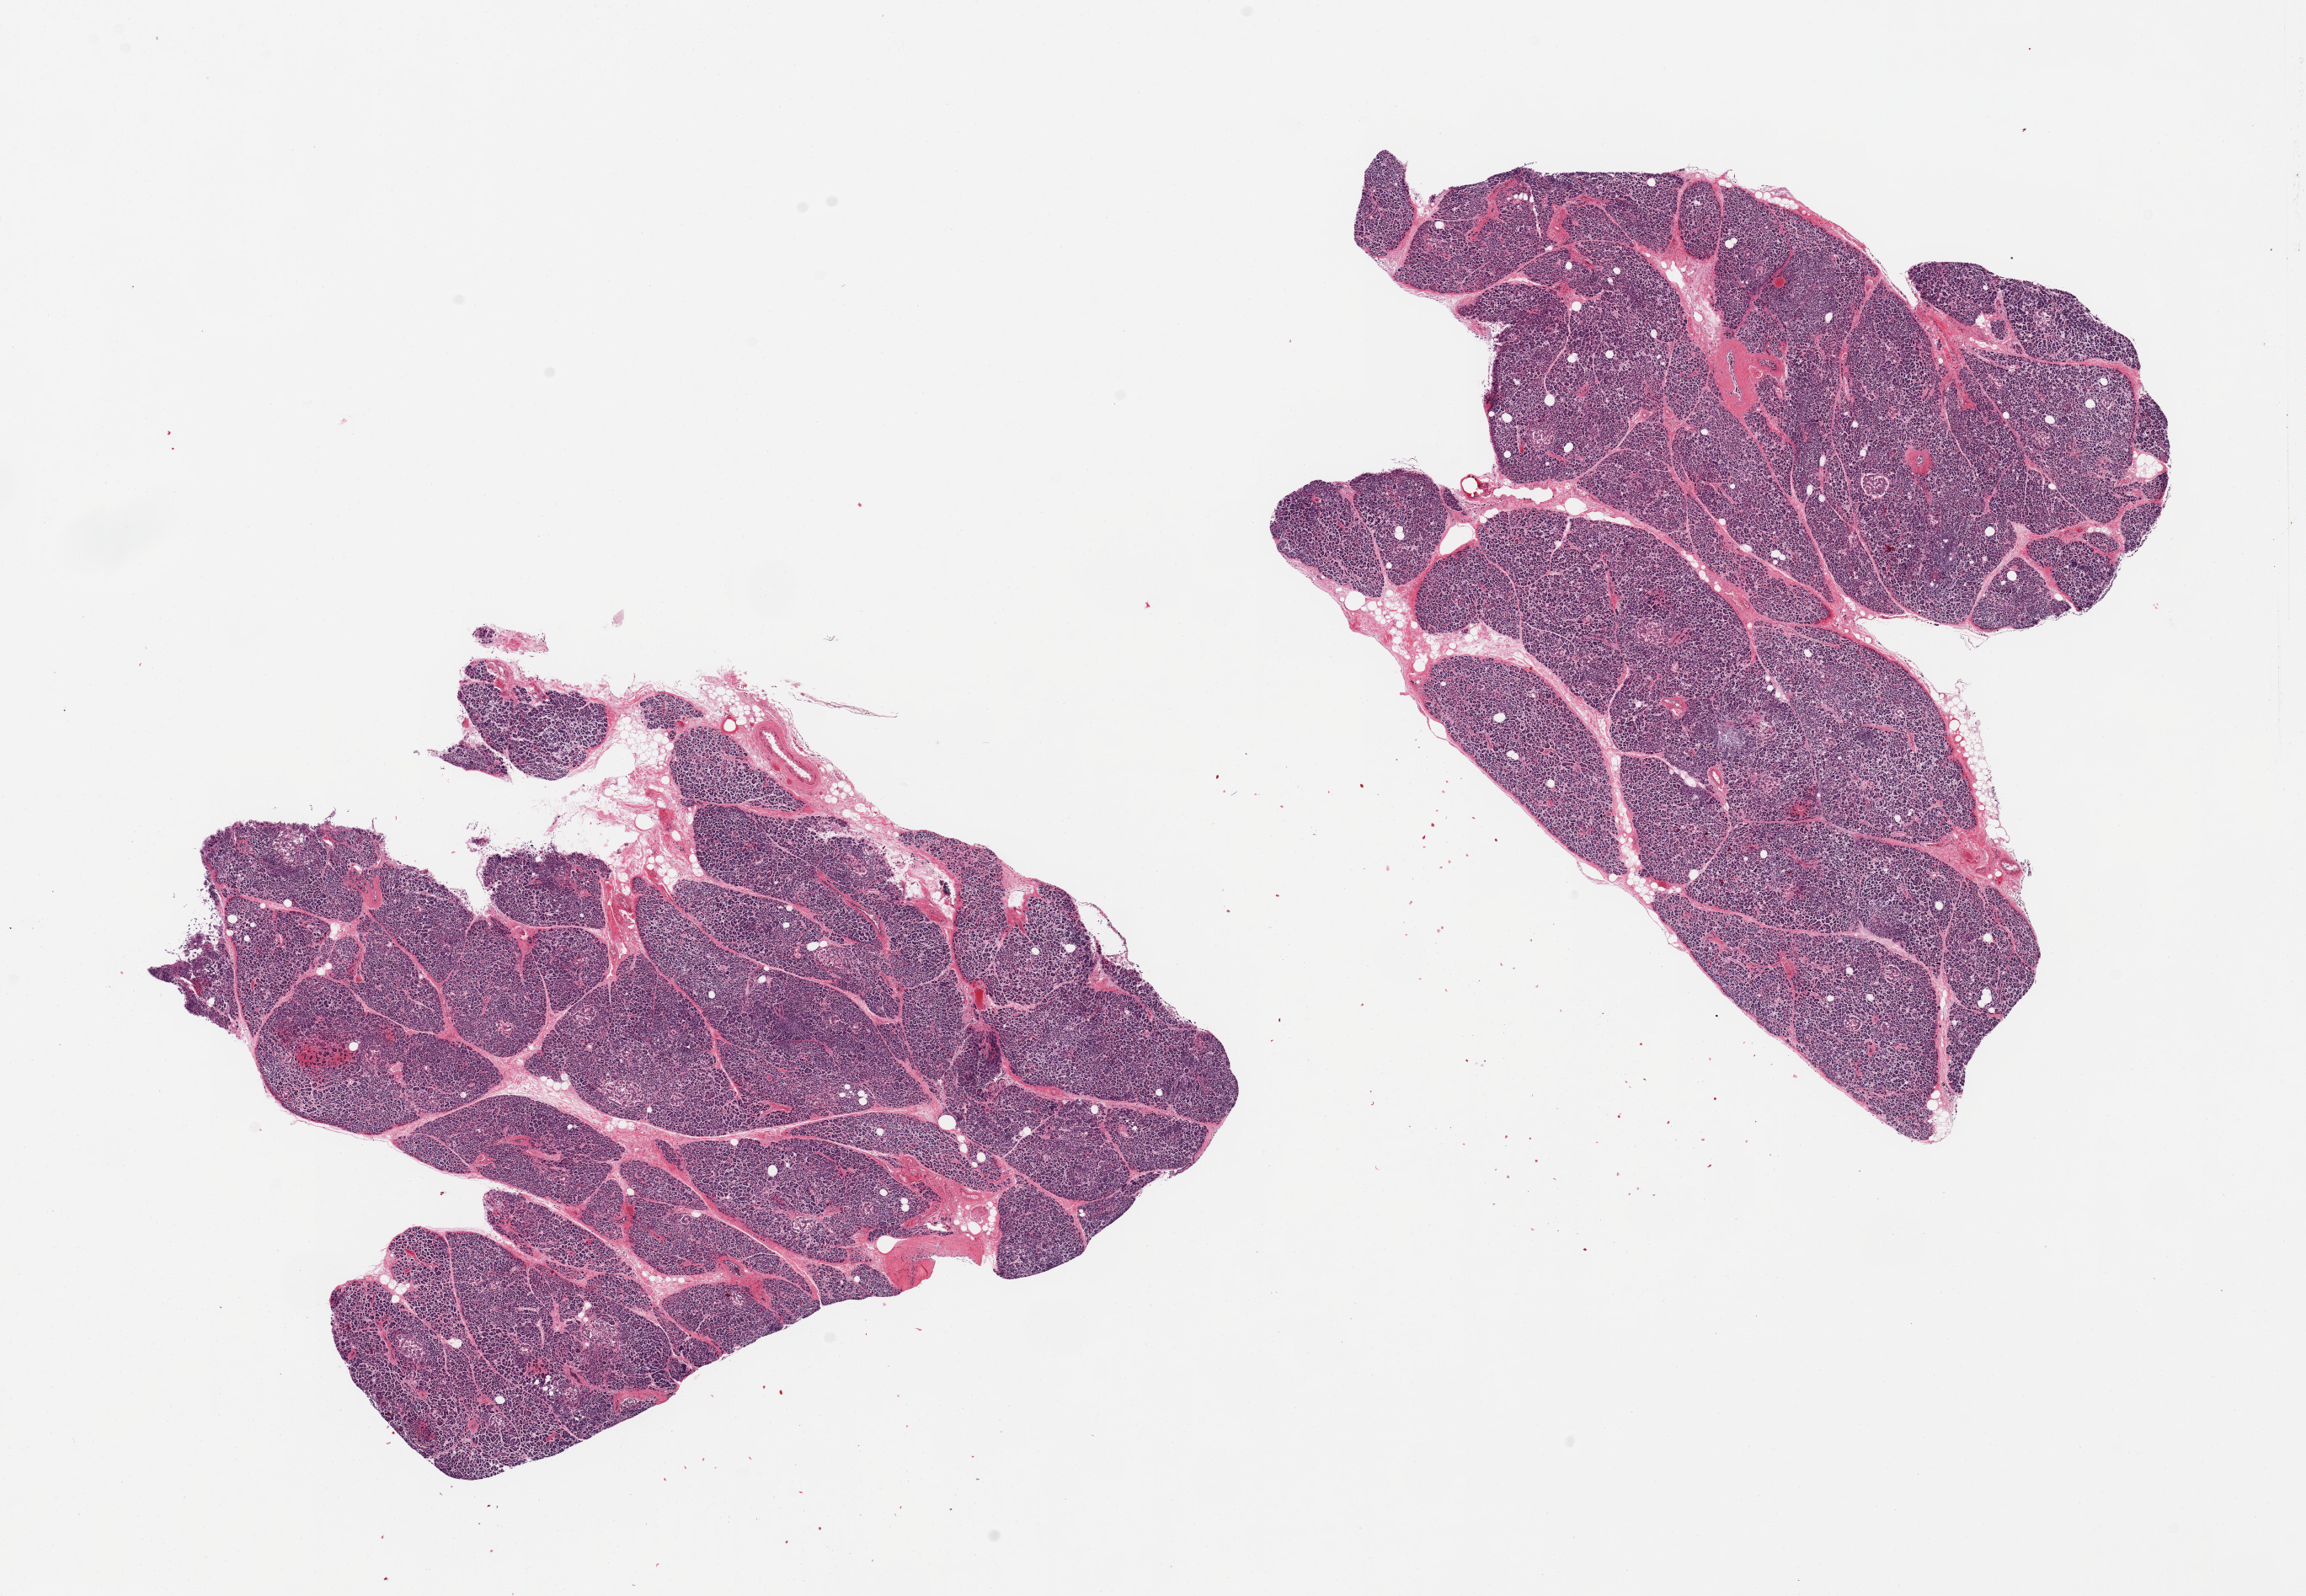
Digitized hematoxylin and eosin (H&E)-stained section — shown as a low-resolution overview of the whole scanned area (about 21.7 x 15.0 mm); PAXgene-fixed, paraffin-embedded tissue; target tissue: pancreas; donor tissue sample. Donor sex: female.
- pathologist's review note for this sample: 2 pieces, moderate autolysis/saponification; Some Islets still visible but degenerating